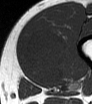
MRI of an extremity soft-tissue mass, one axial slice. Position 18 of 62 along the scan axis. MR volume resampled by the dataset authors to the PET/CT grid (not the native acquisition matrix). 3.27 mm slice thickness. 92 × 104 image matrix. Male patient. From the clinical record (not read from this slice): histological type: mixoid liposarcoma; grade: low; site of the primary tumour: left thigh.
Annotated regions visible in this slice (expert contour drawn on MRI and transferred to this co-registered scan by the dataset authors):
- gross tumour volume (mass): box from (x=25, y=26) to (x=67, y=84) px